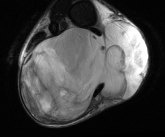
MRI of an extremity soft-tissue mass, one axial slice; position 29 of 81 along the scan axis; T2-weighted fat-saturated; MR volume resampled by the dataset authors to the PET/CT grid (not the native acquisition matrix); 165 × 137 image matrix, field of view 161 × 134 mm. Male patient. Case-level facts recorded for this patient, not image findings: histological type: liposarcoma - round cell; grade: high; site of the primary tumour: right calf.
Annotated regions visible in this slice (expert contour drawn on MRI and transferred to this co-registered scan by the dataset authors):
- gross tumour volume (mass): box from (x=19, y=18) to (x=149, y=120) px